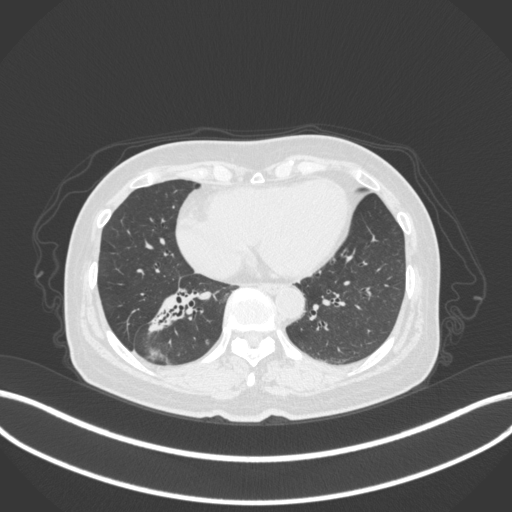
Chest CT, one axial slice. Slice 142 of 429 in the series (ordered by position). Reconstruction kernel B31f. 120 kVp. Lung window (W 1500 / L -600 HU). 1 mm slice thickness. 512 × 512 image matrix, field of view 400 × 400 mm. Female patient, age 67 years. Case-level facts recorded for this patient, not image findings: clinical TNM (as recorded): T1c N1 M0; histopathological grade: G2-3.
Structures marked on this image (bounding box drawn by a radiologist):
- lung tumour (recorded histology: adenocarcinoma): bounding box (x1, y1, x2, y2) in pixels: (139, 286, 201, 336)